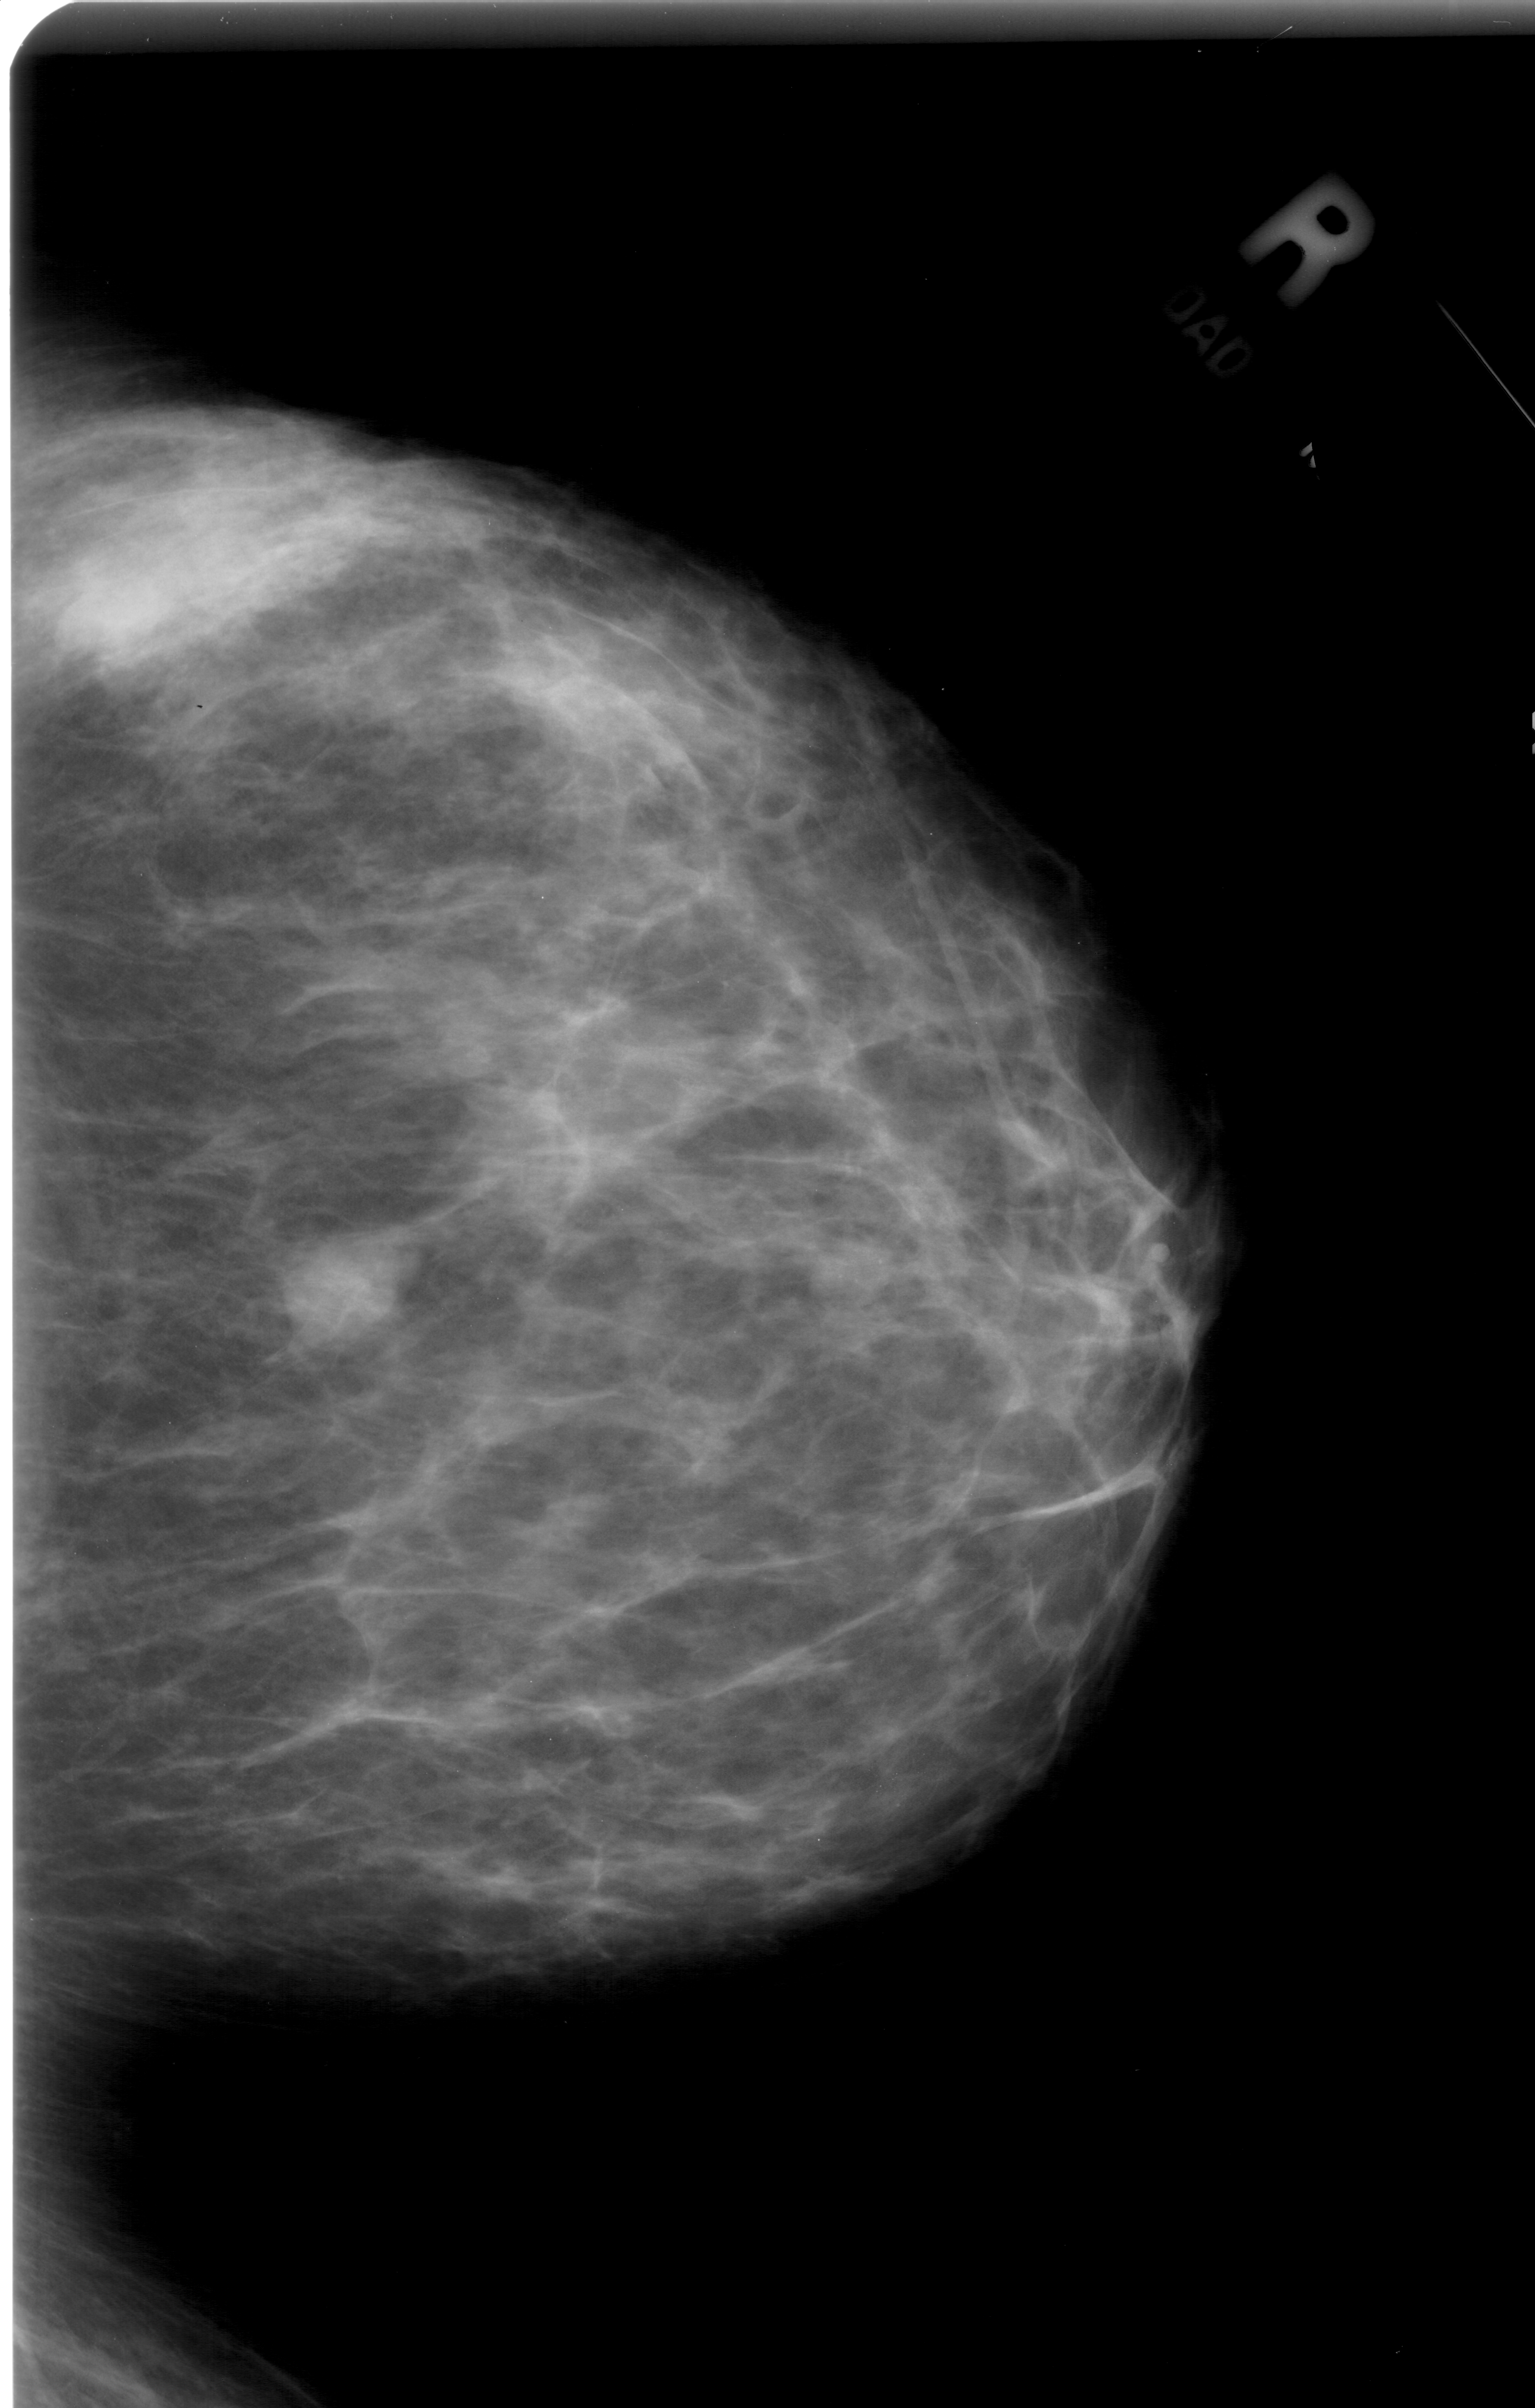
Mammogram (digitized film), right breast, CC view, BI-RADS breast density category 1 (scale 1–4).
Finding: mass, shape lobulated, margins ill defined; BI-RADS assessment category 4; subtlety rating 3 on a 1 (subtle) to 5 (obvious) scale; pathology (as recorded): benign.